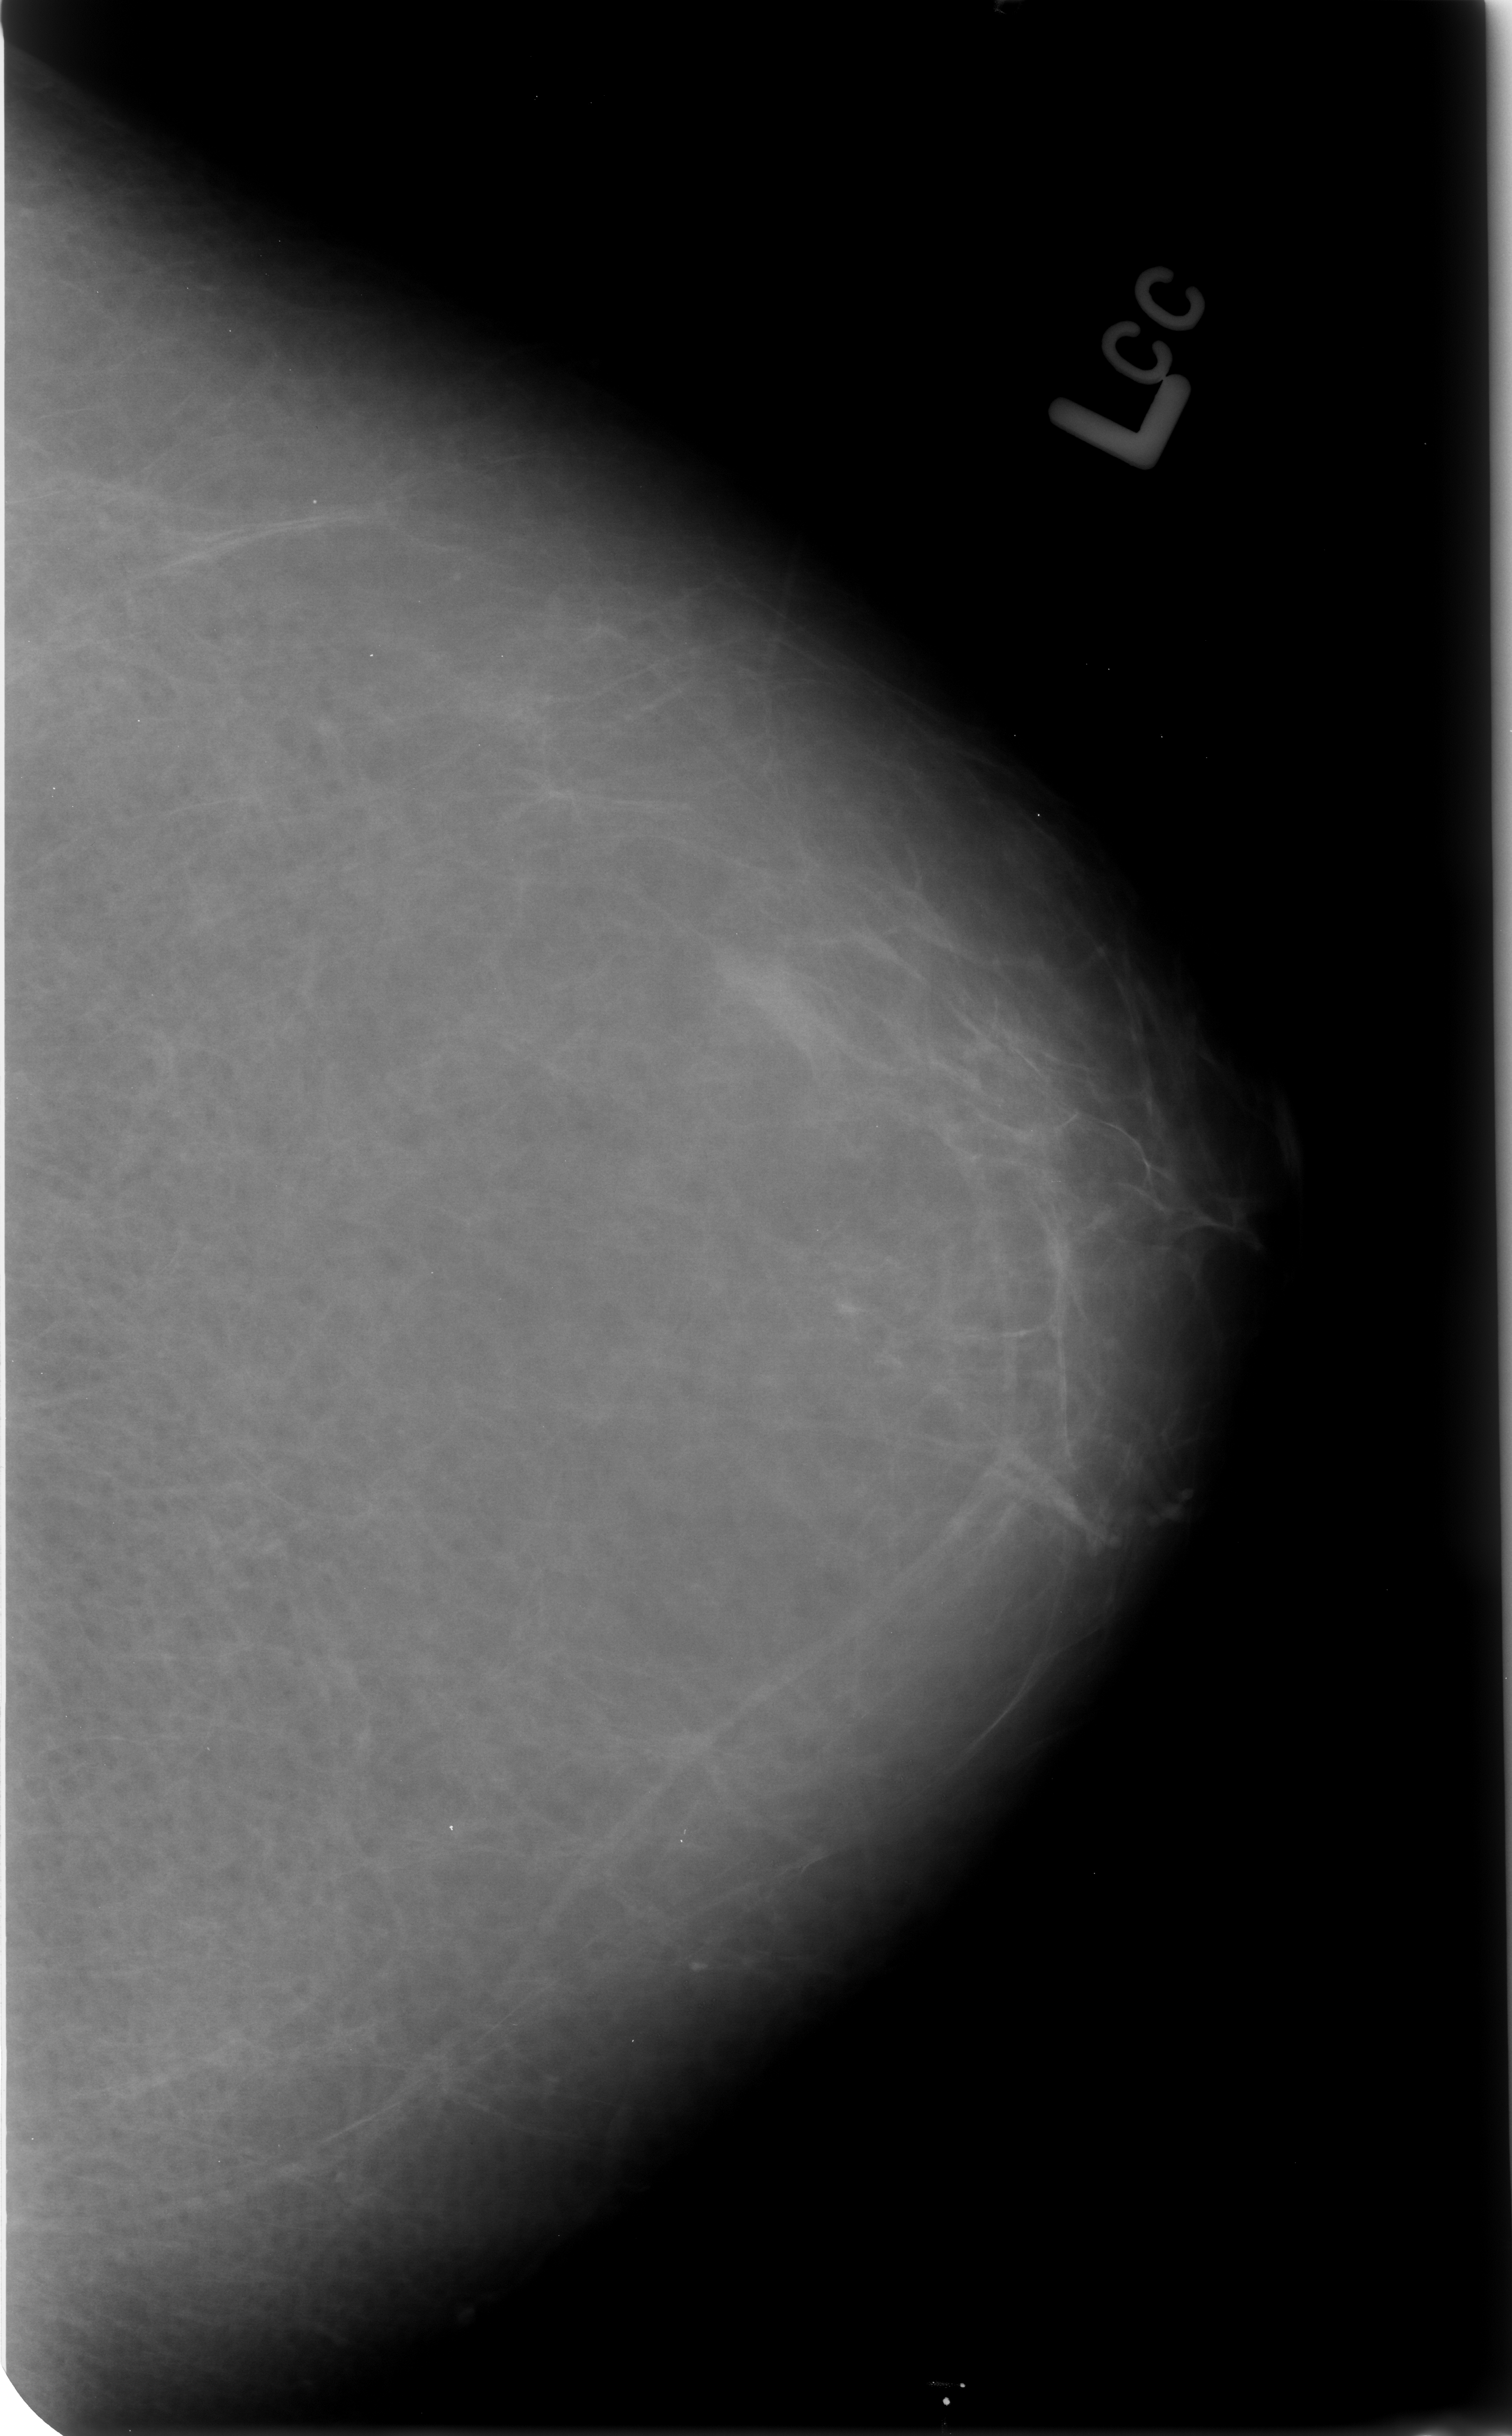
Digitized screen-film mammogram. Left breast. Craniocaudal (CC) view. BI-RADS breast density category 1 (scale 1–4). 1512 × 2436 image matrix.
Marked abnormalities (boxes around the expert regions of interest):
- mass, shape irregular, margins ill defined; BI-RADS assessment category 4; subtlety rating 4 on a 1 (subtle) to 5 (obvious) scale; pathology result (as recorded, not read from the image): benign: box from (x=713, y=939) to (x=840, y=1058) px